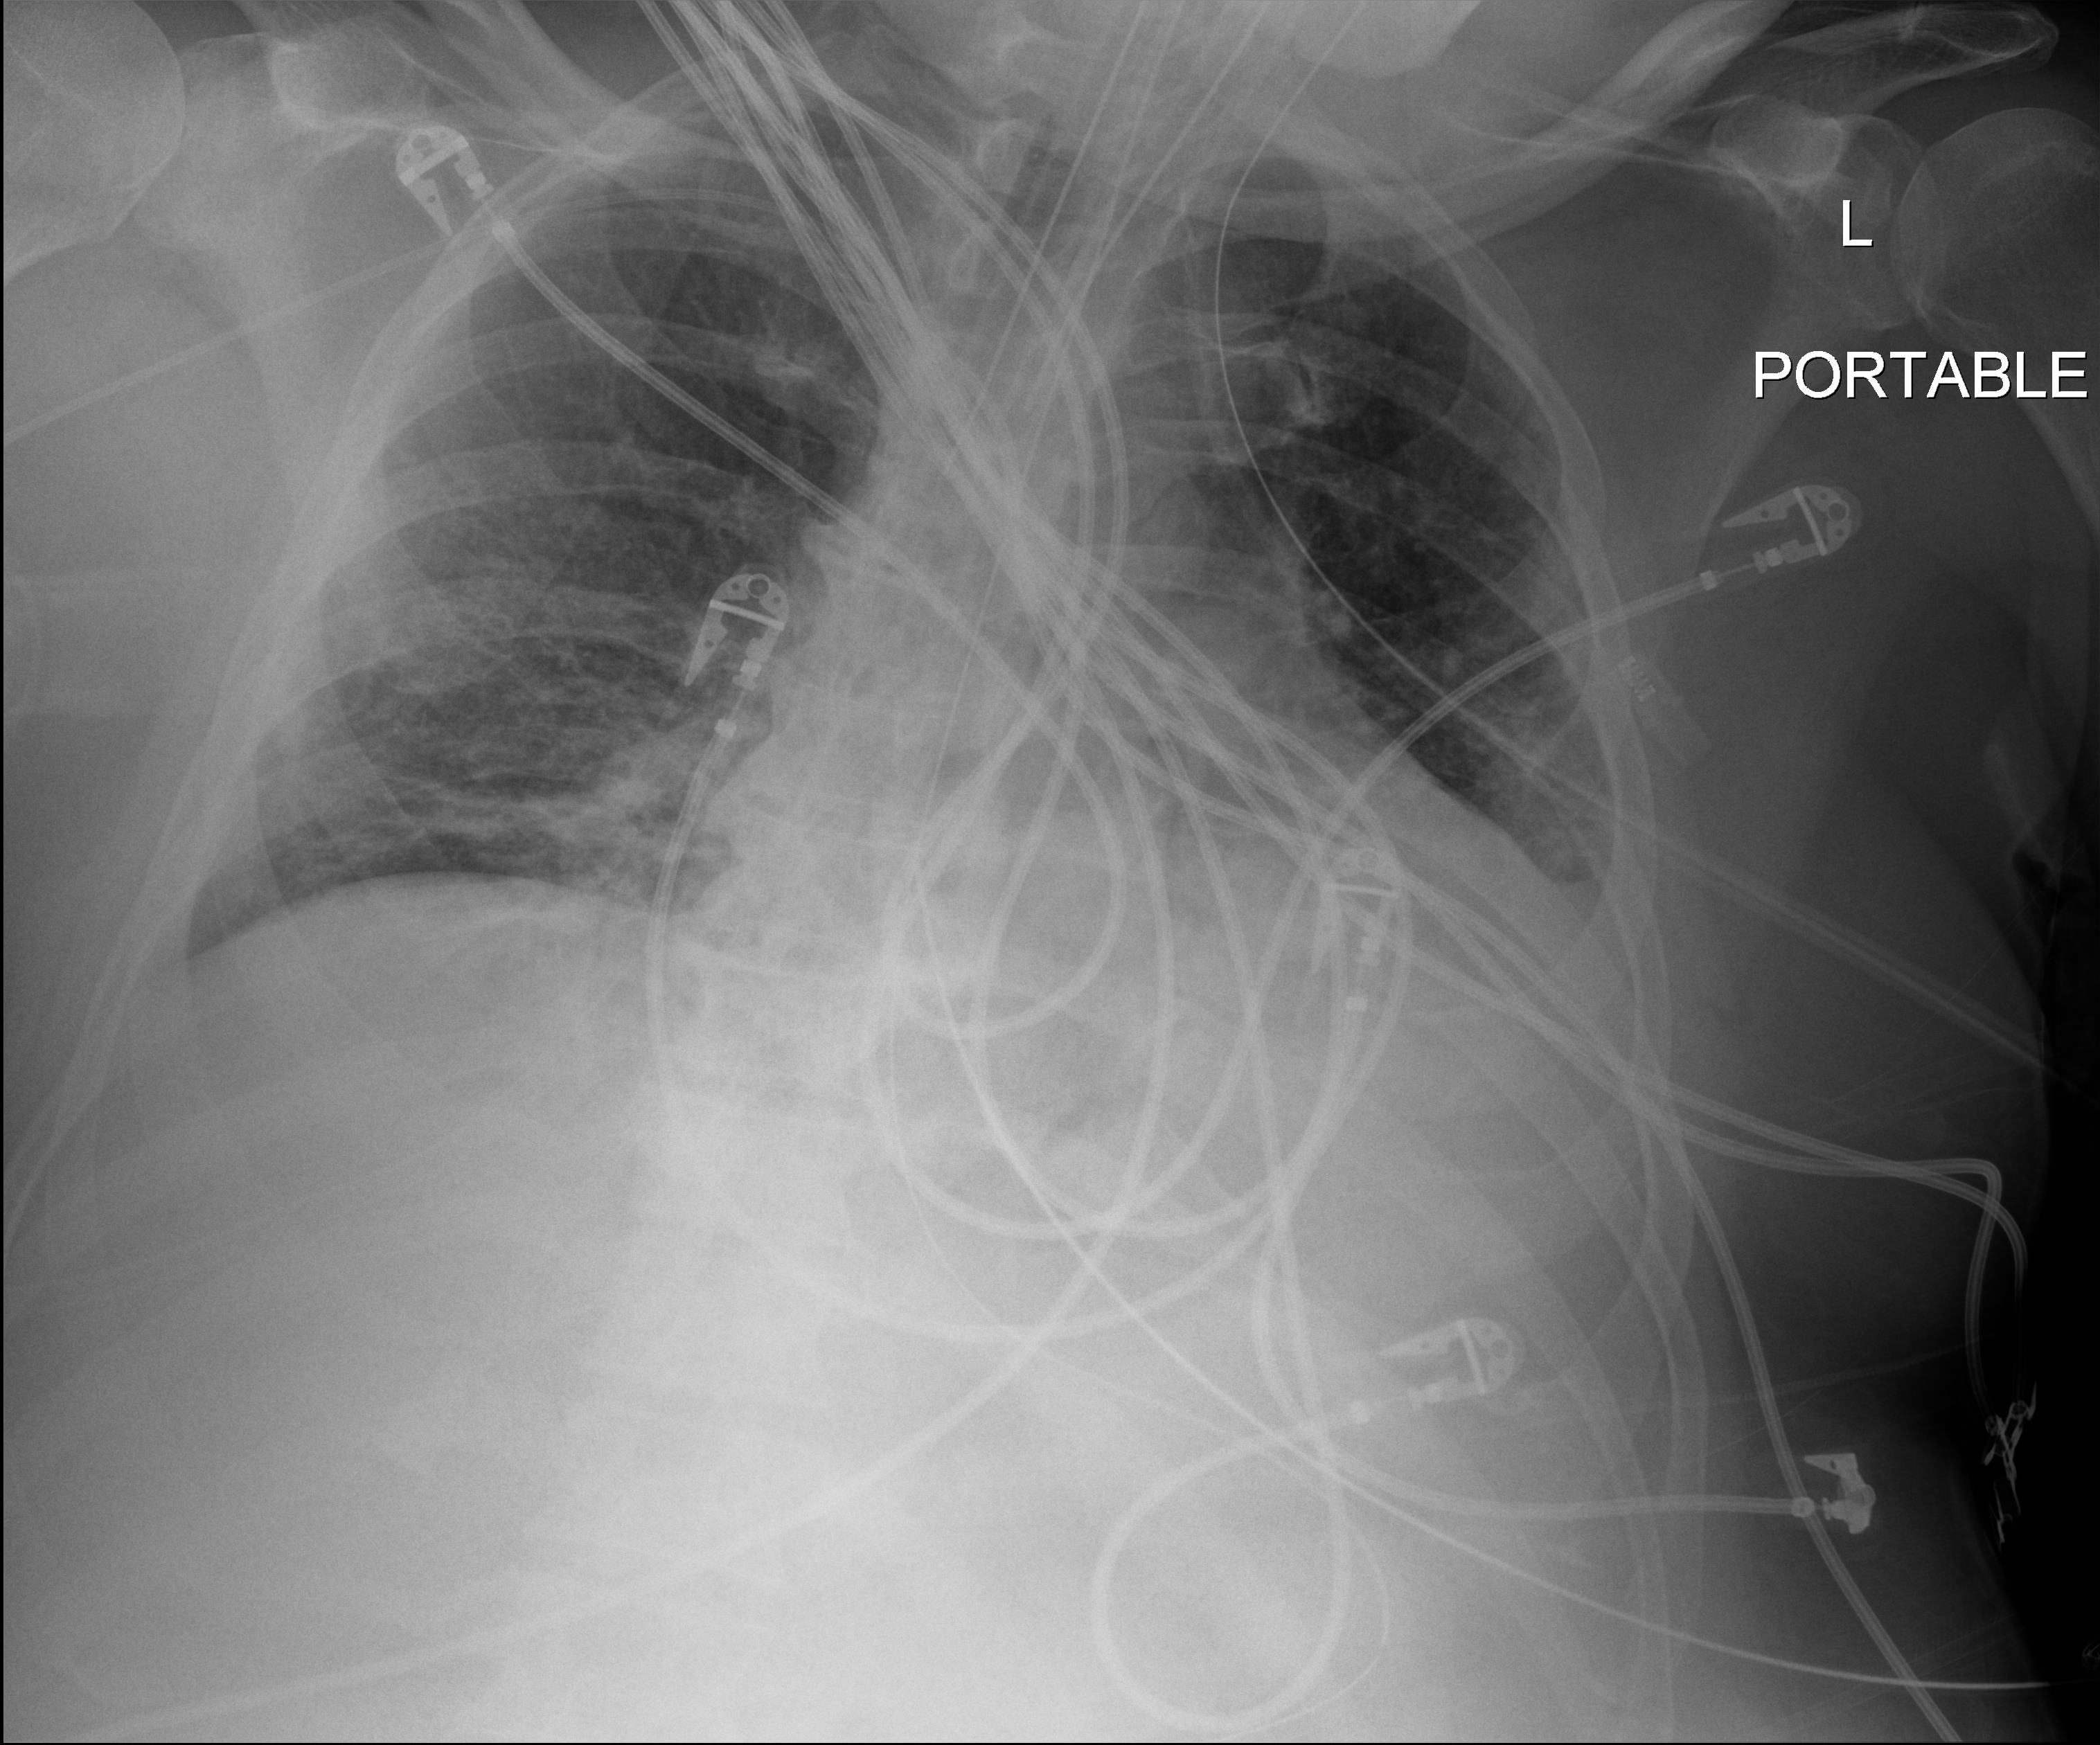
Bedside chest radiograph (digital radiography); anteroposterior (AP) projection. Male patient hospitalised with COVID-19, age 18–59 years.
Hospital-stay facts (about this admission, not read from this image; timing relative to this image not recorded): admitted to intensive care during this hospital stay: yes.